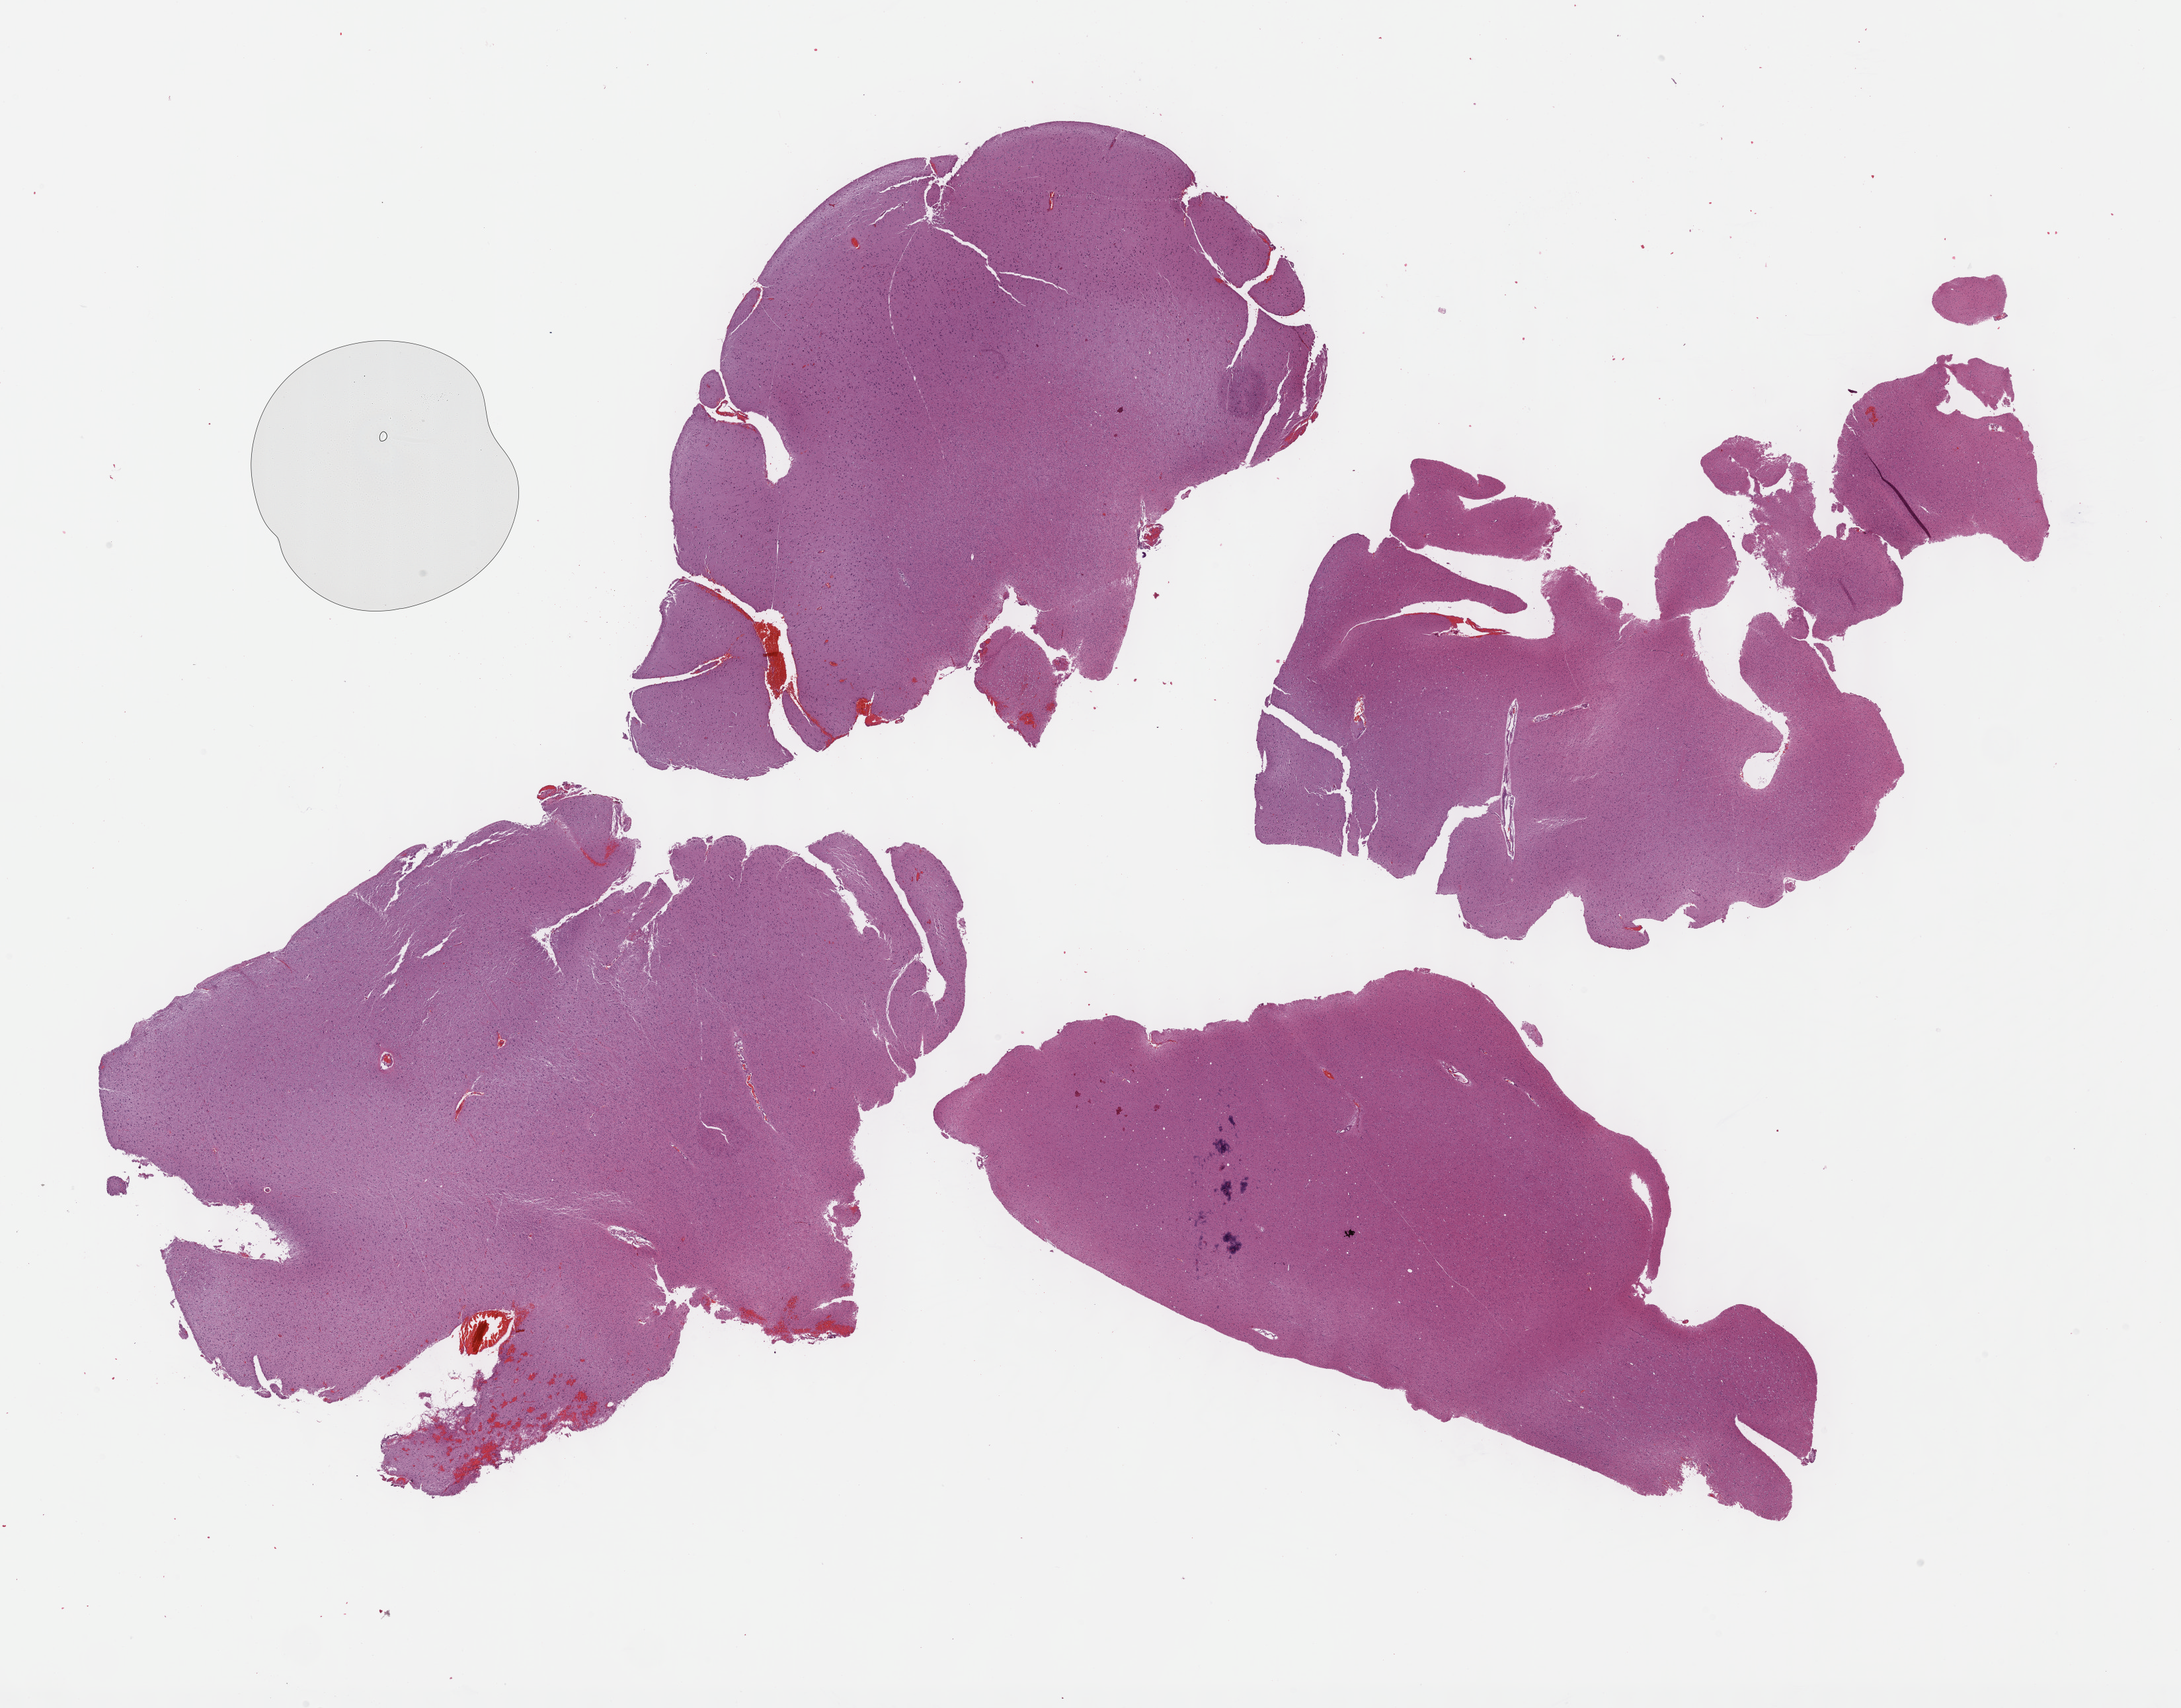
Digitized H&E tissue section (whole slide), a low-resolution overview of the entire scanned area, about 26.7 x 20.9 mm (acquisition: 40x scan). Formalin-fixed paraffin-embedded (FFPE) diagnostic section. Brain, primary tumour sample. Male patient; age at initial diagnosis 38 years. Histologic grade: G2 (moderately differentiated).
Histologic diagnosis: Oligodendroglioma, NOS.